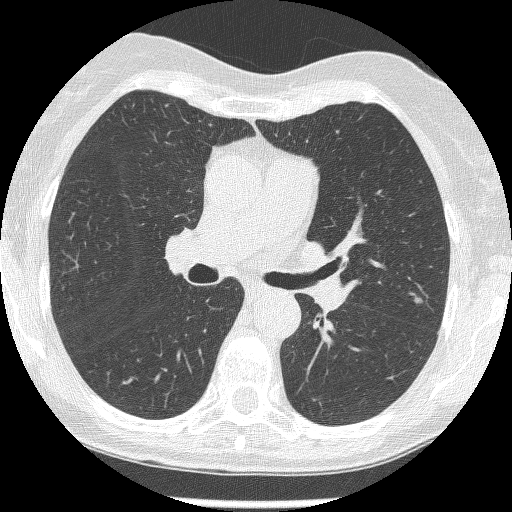
Axial slice from a low-dose chest CT screening exam; second screening round (one year after baseline); lung window (W 1500 / L -600 HU); 1.25 mm slice thickness; lung (sharp) reconstruction kernel (BONE). Female participant, aged 60 years at enrolment. Current smoker at enrolment.
Expert-annotated lung lesion, box from (x=399, y=284) to (x=439, y=318) px. The screening reader recorded 2 non-calcified nodules or masses ≥4 mm on this exam (left upper lobe, left upper lobe); which of them this box marks is not recorded. Lung cancer was diagnosed 428 days after this screen: adenocarcinoma, NOS, left upper lobe, moderately differentiated (G2), stage IA (AJCC 6th edition), 6 mm at pathology.